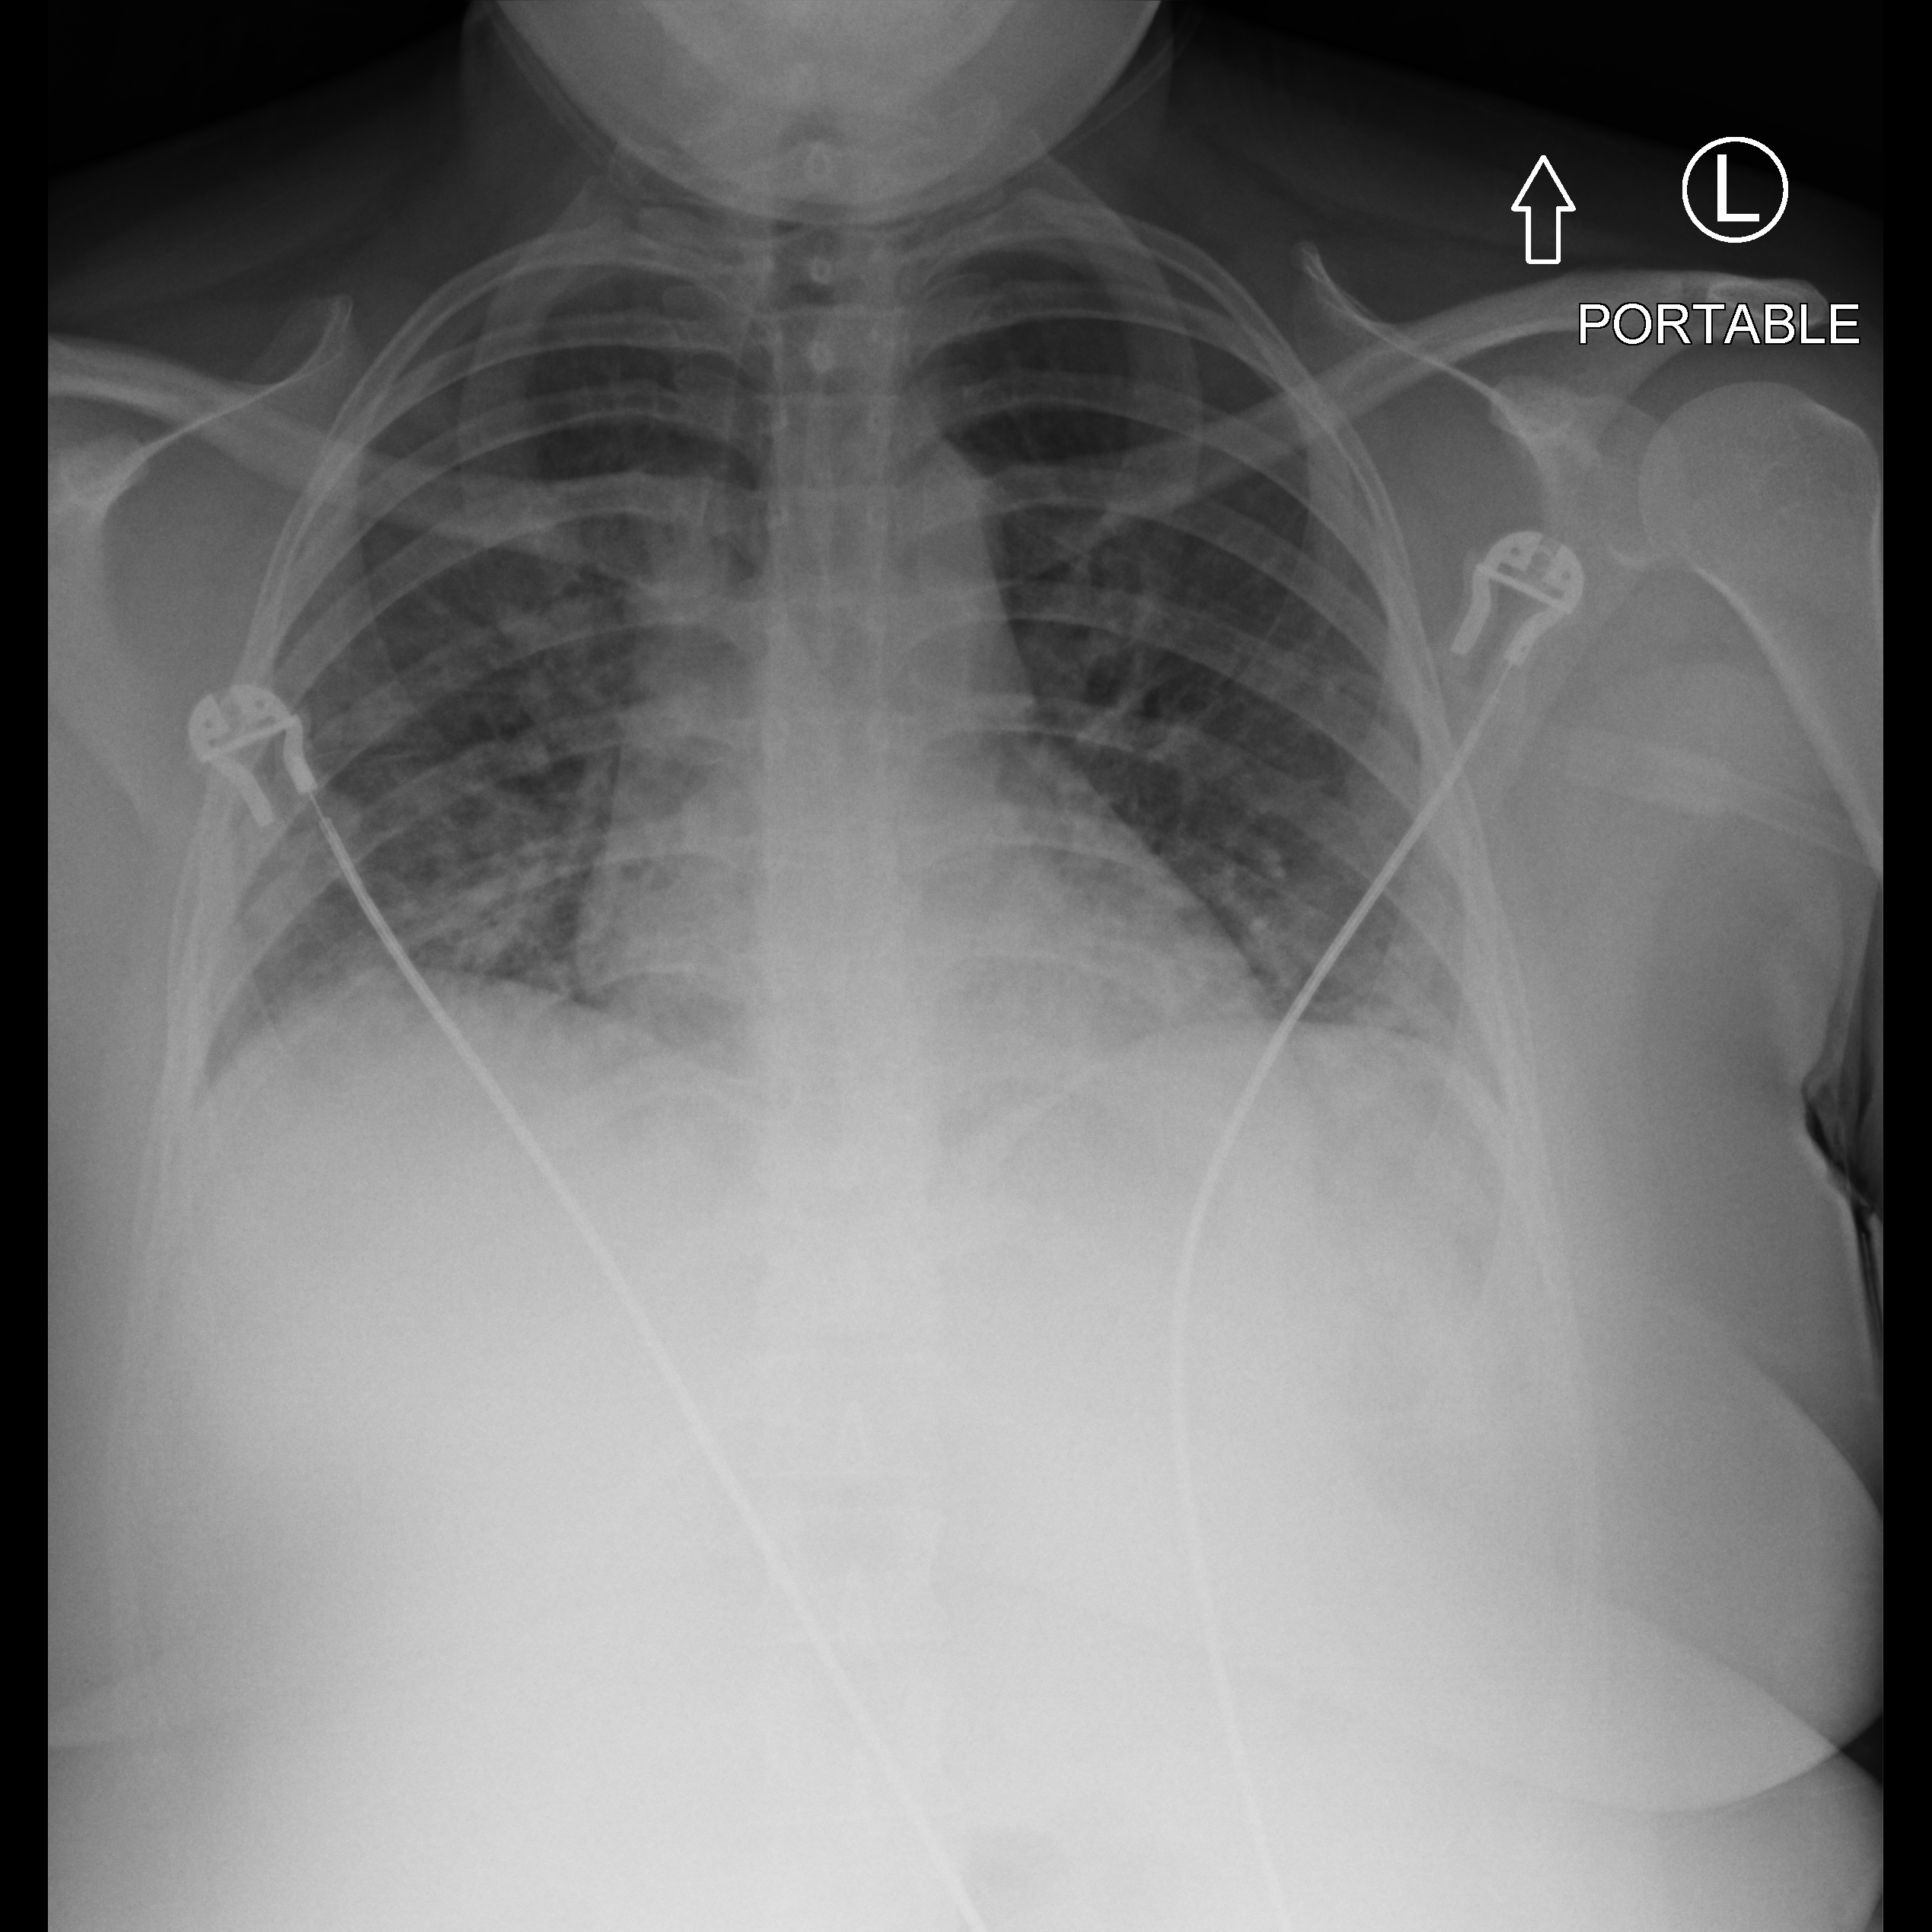
Bedside chest radiograph (computed radiography). Female patient hospitalised with COVID-19, age 18–59 years.
From the hospital-stay record, not from the radiograph (when in the stay this image was taken is not recorded):
- other chronic lung disease (admission record): yes
- mechanically ventilated during this hospital stay: no
- admitted to intensive care during this hospital stay: no